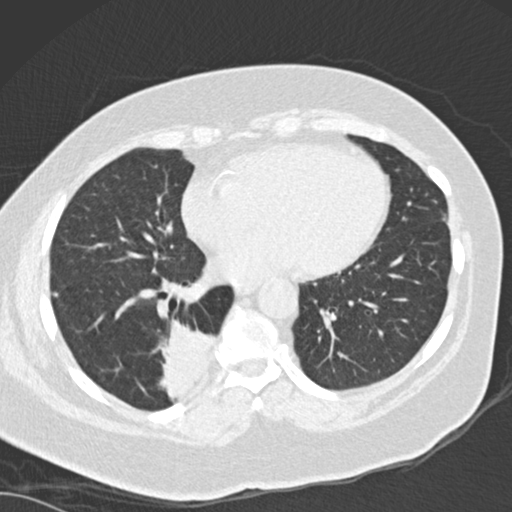
Low-dose screening chest CT, one axial slice; slice 63 of 162 in the series (ordered by position); reconstruction kernel B30f; 120 kVp; lung window (W 1500 / L -600 HU); 2 mm slice thickness; 512 × 512 image matrix, field of view 328 × 328 mm.
Structures marked on this image (outlined manually by an expert reader):
- lesion 1 (tumor, lower lobe of right lung): bounding box [x1, y1, x2, y2] px = [156, 319, 218, 403]